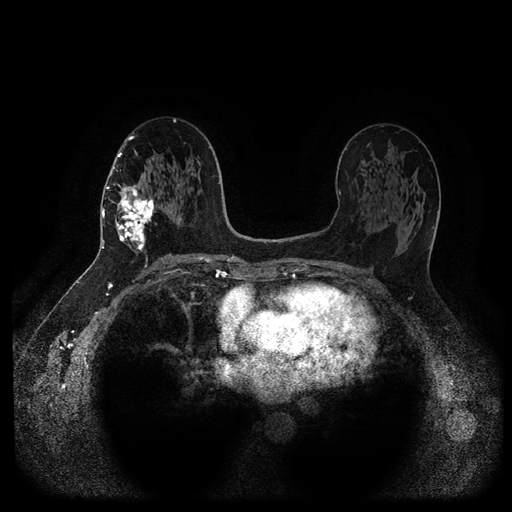
Breast MRI (dynamic contrast-enhanced, multi-phase), one axial slice; position 56 of 116 along the scan axis; dynamic contrast-enhanced series, time point 2 of 5 at this slice position (early post-contrast); 1.5 T; TE 2.6 ms, TR 5.3 ms; 2 mm slice thickness; 512 × 512 image matrix, field of view 360 × 360 mm. Patient: female, 58 years.
Outlined on this slice (semi-automatic segmentation, software-assisted and operator-edited):
- breast lesion (labelled 'tumour' in the annotation; benign lesions carry a separate 'benign' label): bounding box (x1, y1, x2, y2) in pixels: (114, 183, 156, 255)